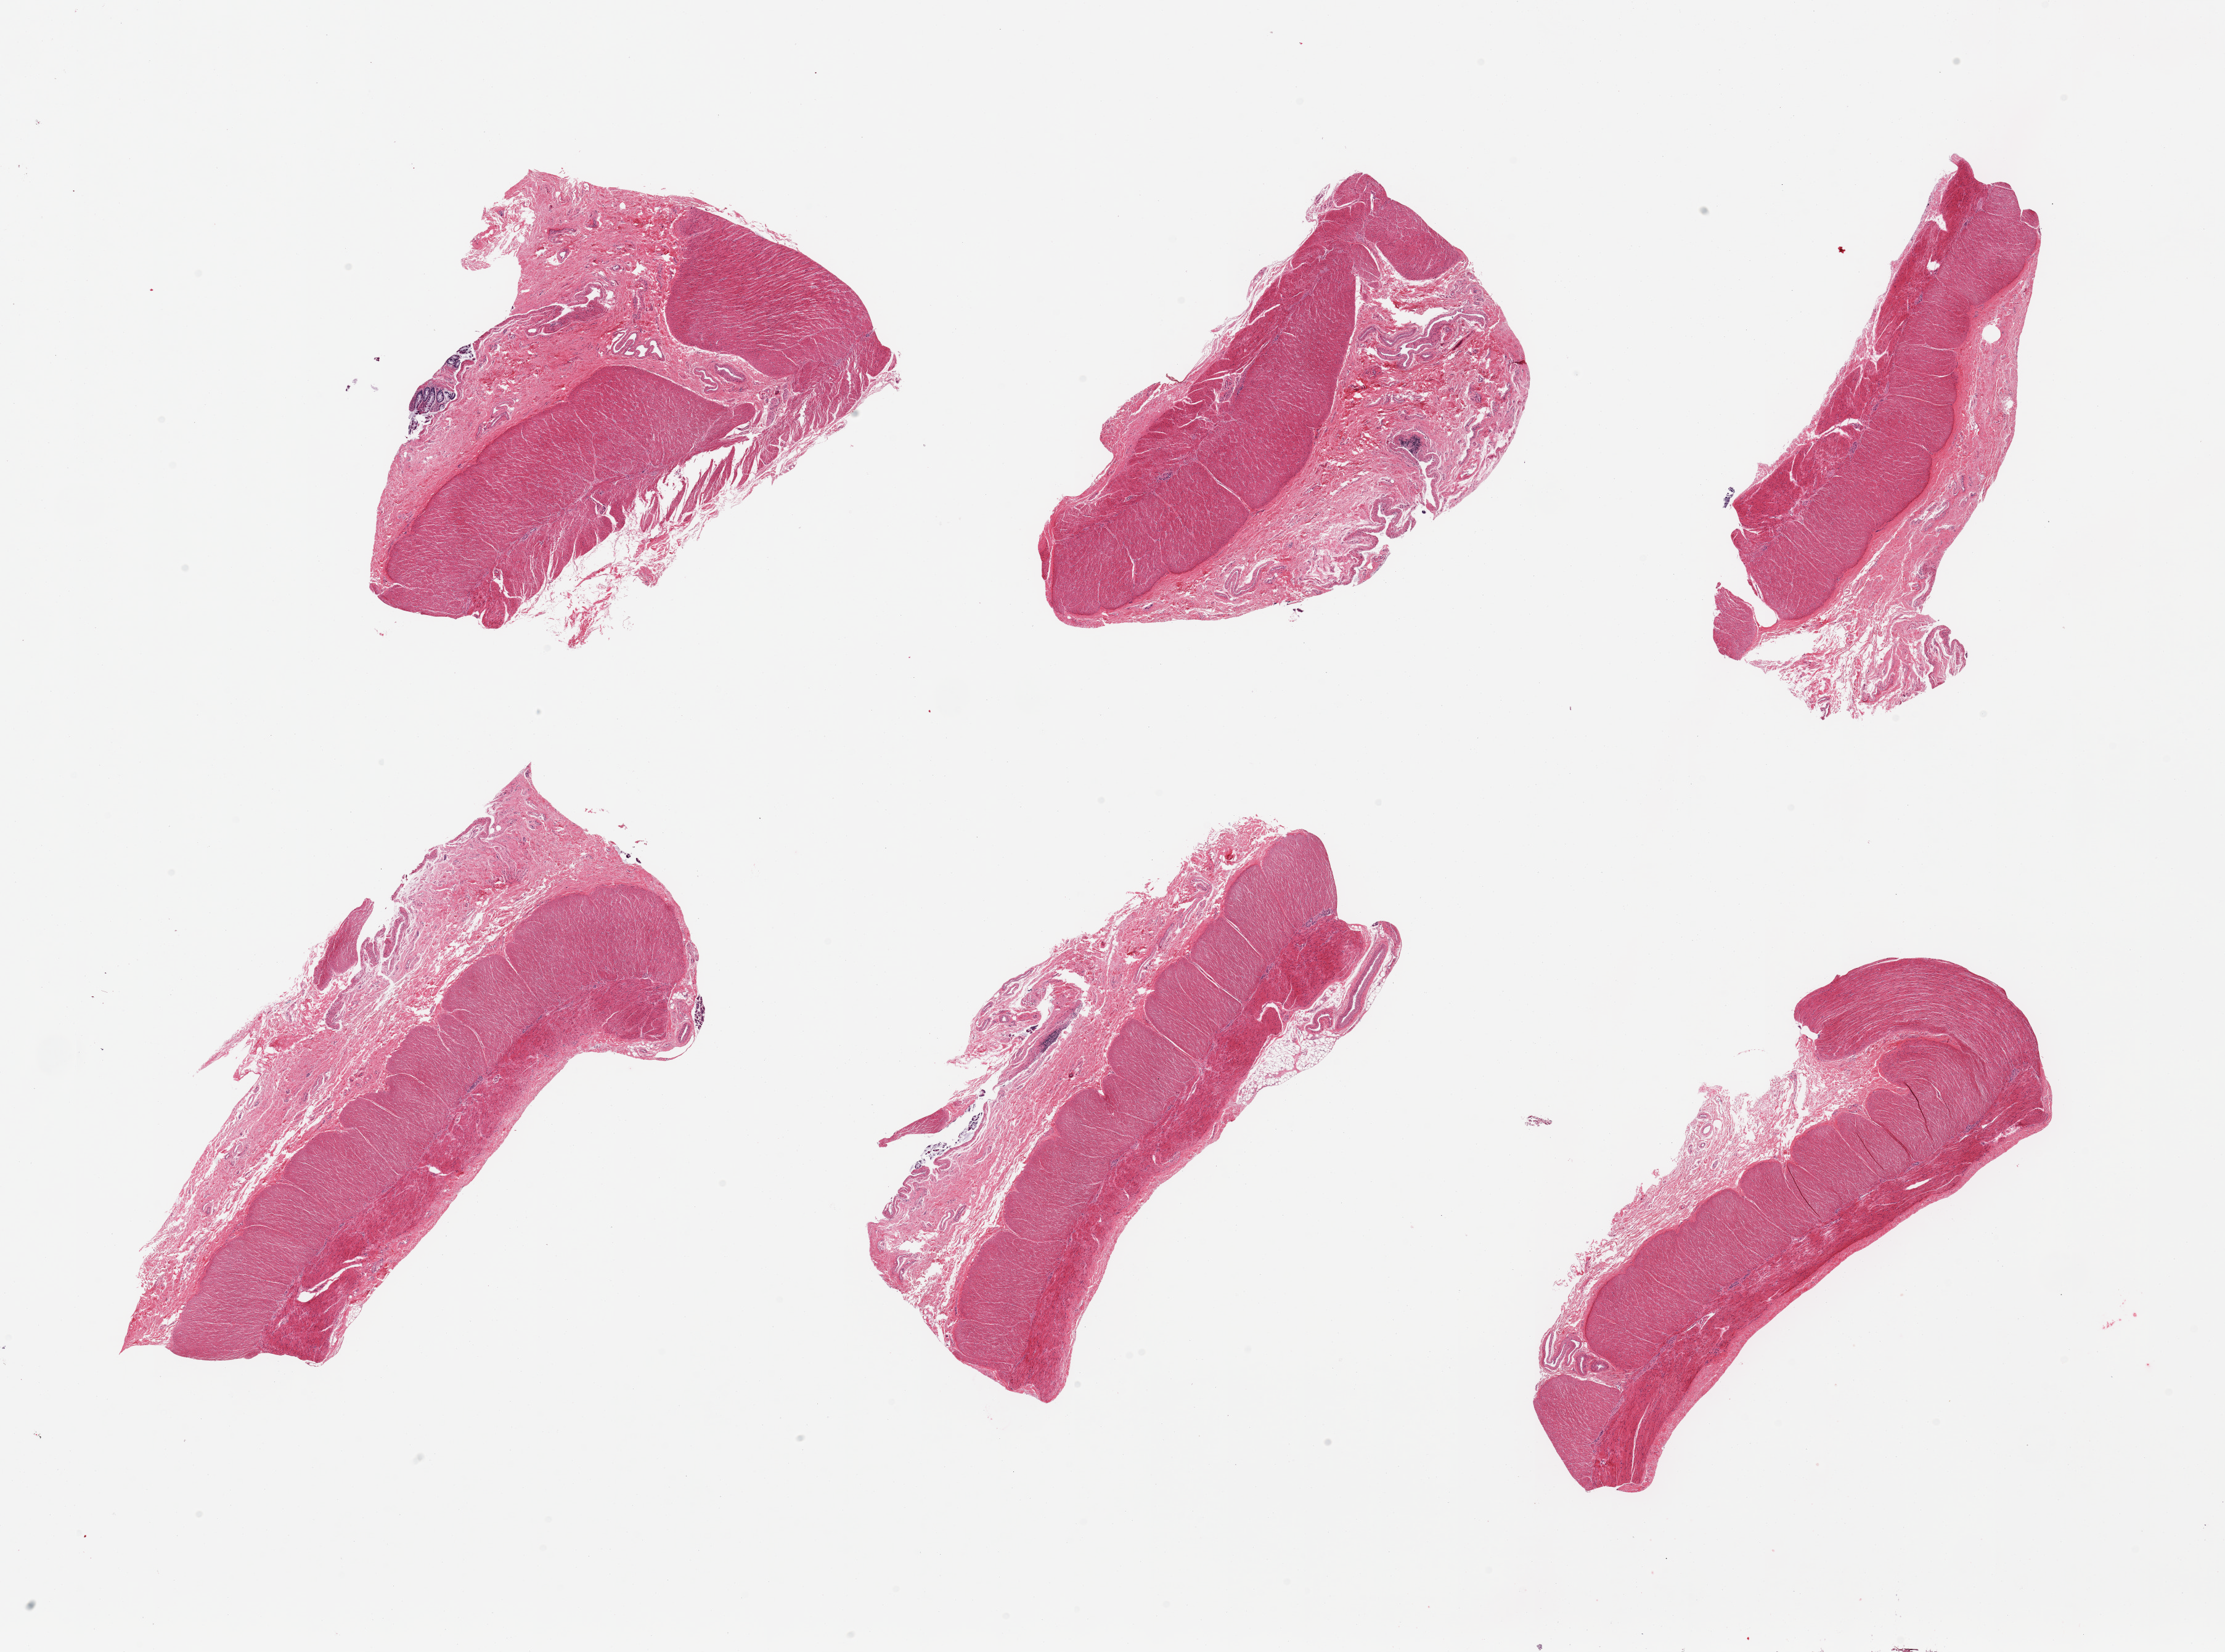
Haematoxylin and eosin whole-slide image, whole scanned area (about 28.5 x 21.2 mm, from a 20x scan) shown as a low-resolution overview; PAXgene-fixed, paraffin-embedded tissue; section of sigmoid colon (target tissue); tissue donor sample. Male donor.
* pathologist's review note for this sample: 6 pieces, all target muscularis